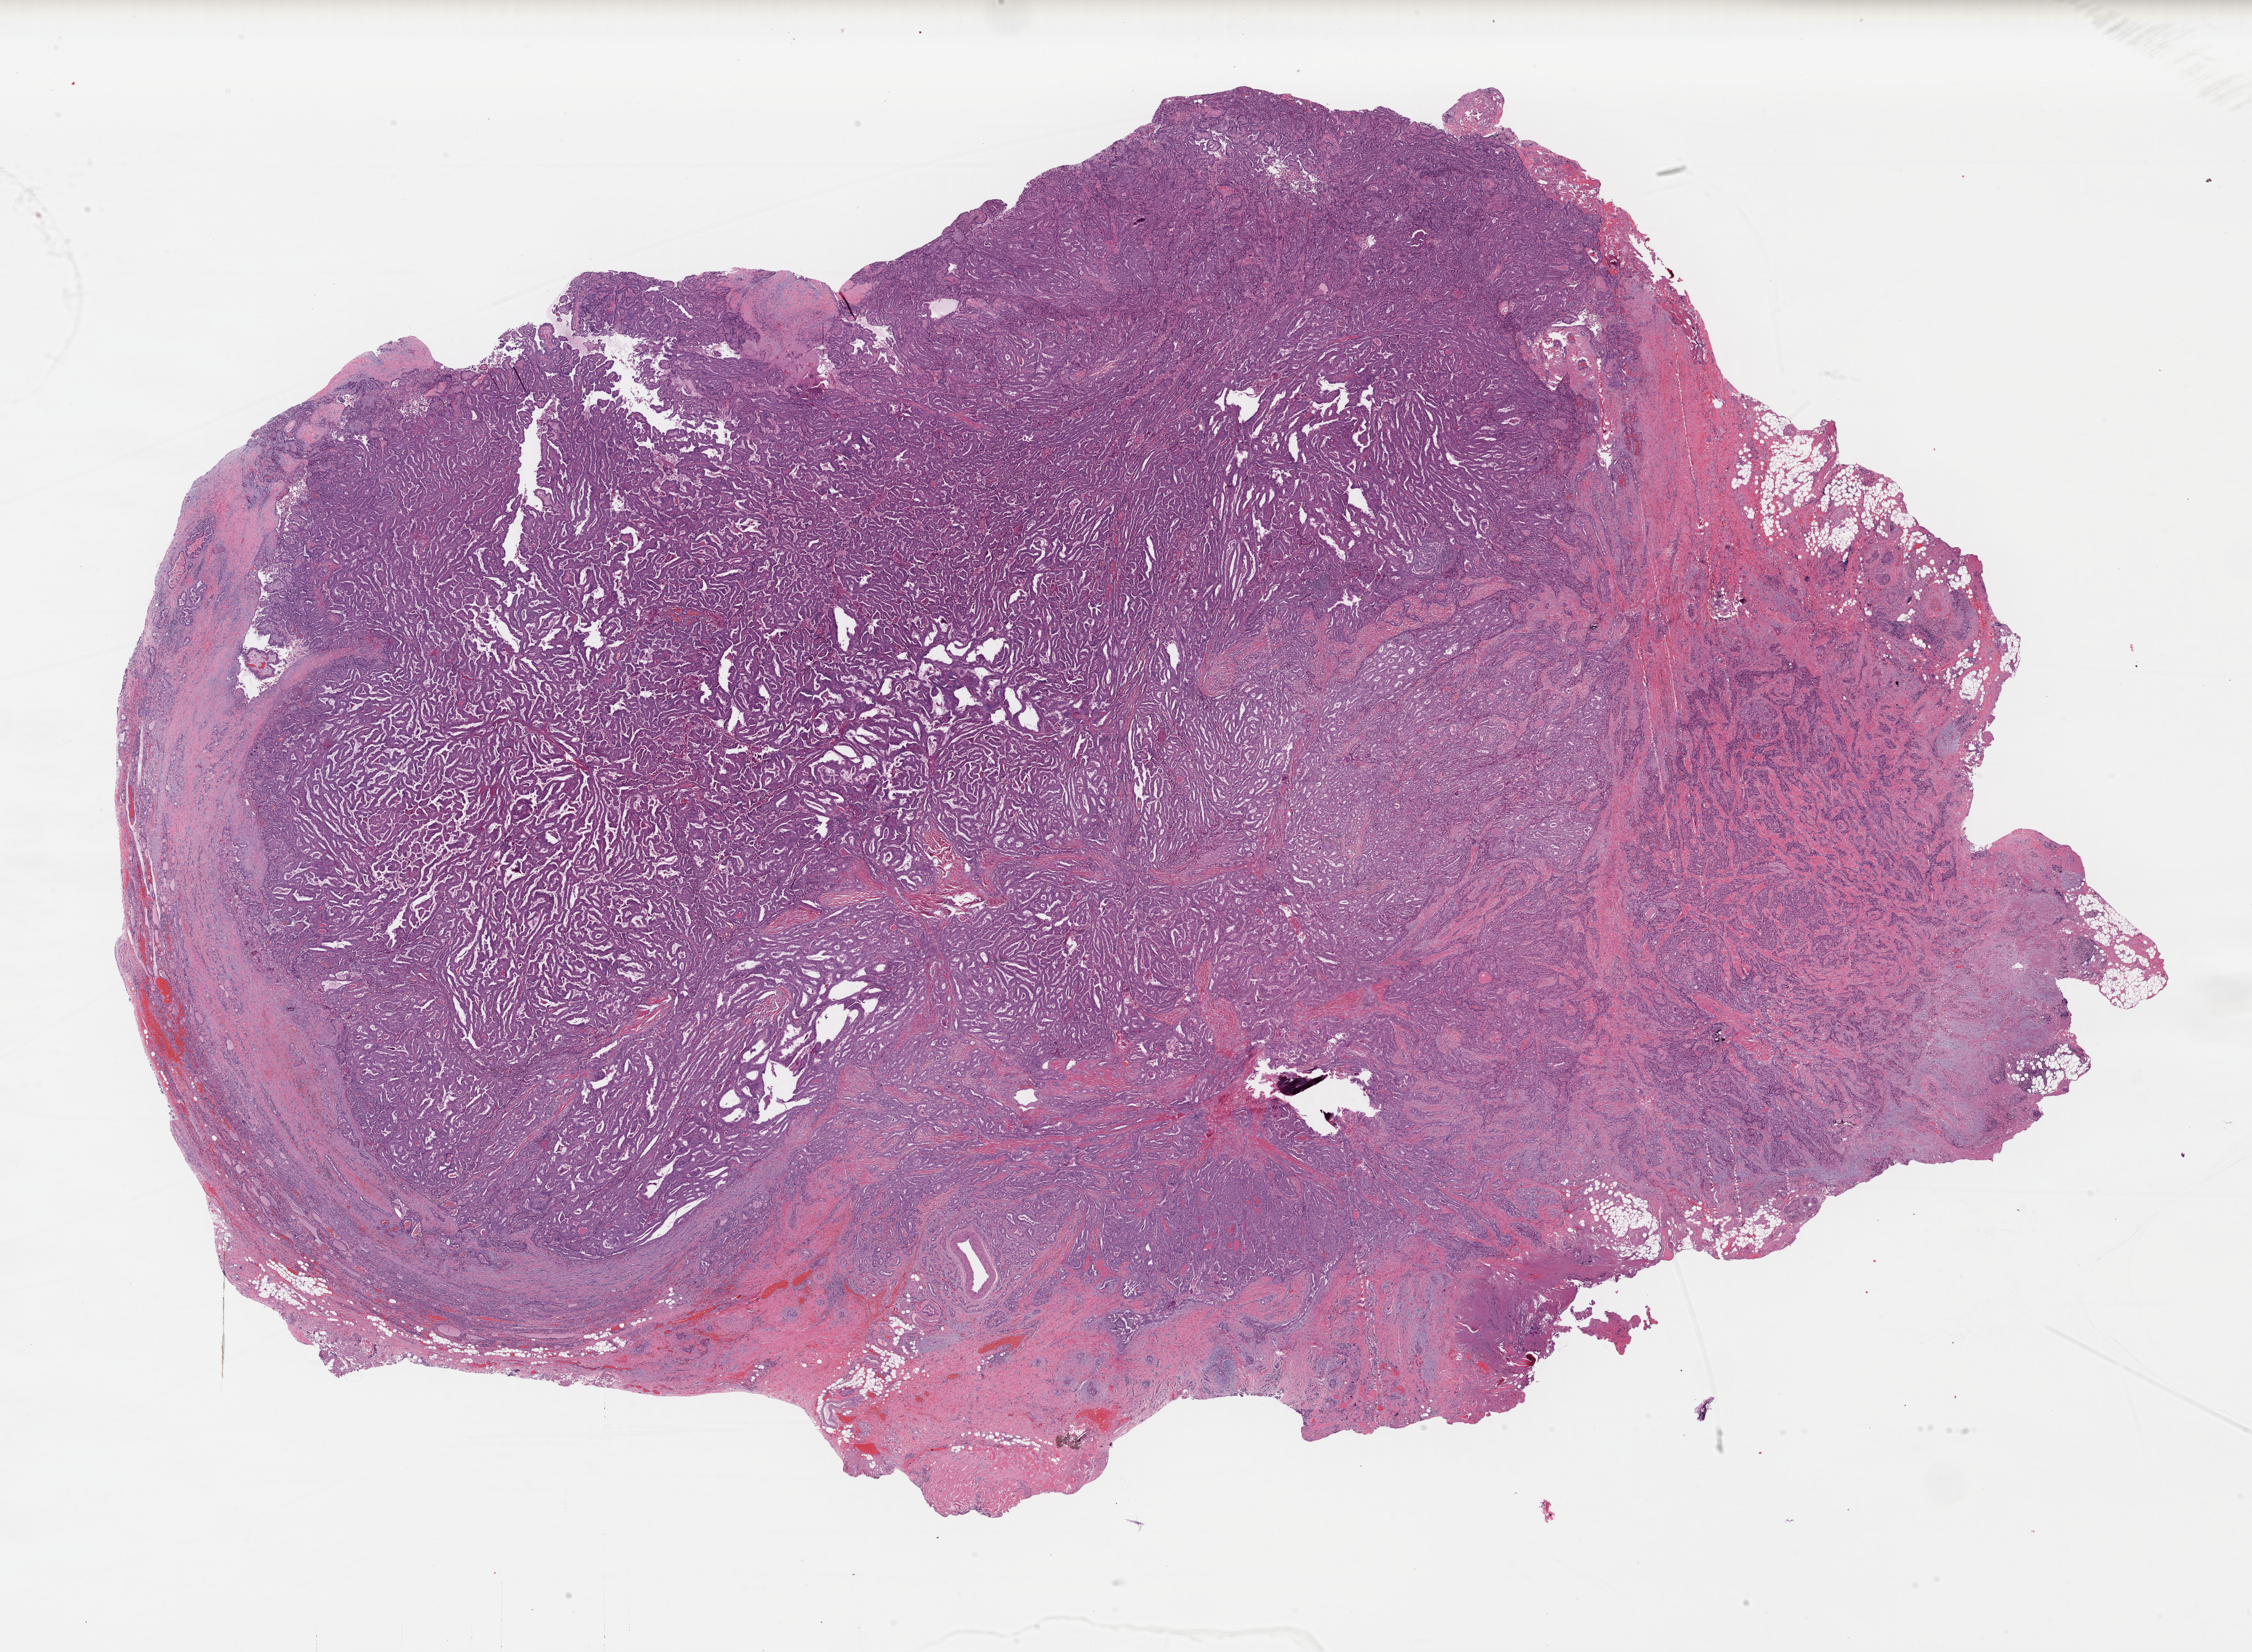
Whole-slide histology image, H&E, low-resolution overview of the scanned area, about 28.8 x 21.1 mm; formalin-fixed paraffin-embedded (FFPE) diagnostic section; sample: primary tumour, thyroid. Patient: female, age at initial diagnosis 24 years.
Laterality: left. Pathologic diagnosis: Papillary adenocarcinoma, NOS. Lymph nodes positive (case pathology): 5 of 27 examined. AJCC pathologic stage: I (7th edition).